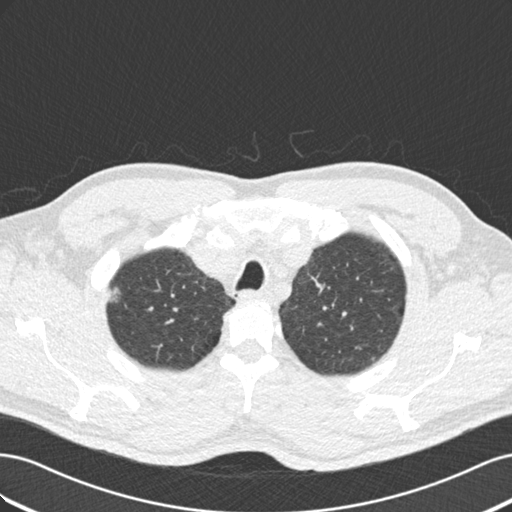
Chest CT (low-dose screening protocol), one axial image; second annual screen; lung window (W 1500 / L -600 HU); standard (soft-tissue) reconstruction kernel (B30f); 512 × 512 image matrix. Male, age 56 years at enrolment.
Expert reader's lesion annotation, bounding box (x1, y1, x2, y2) in pixels: (96, 277, 134, 311). The exam's reader record, not a measurement of the box and not confirmed to be the same lesion: non-calcified nodule or mass ≥4 mm, right upper lobe, 13 × 12 mm, smooth margins, mixed attenuation, pre-existing on the prior screen: yes; interval growth: yes. Later outcome: lung cancer diagnosed 174 days after this screen — bronchiolo-alveolar carcinoma, non-mucinous, right upper lobe, moderately differentiated (G2), stage IIIB (AJCC 6th edition), 10 mm at pathology.